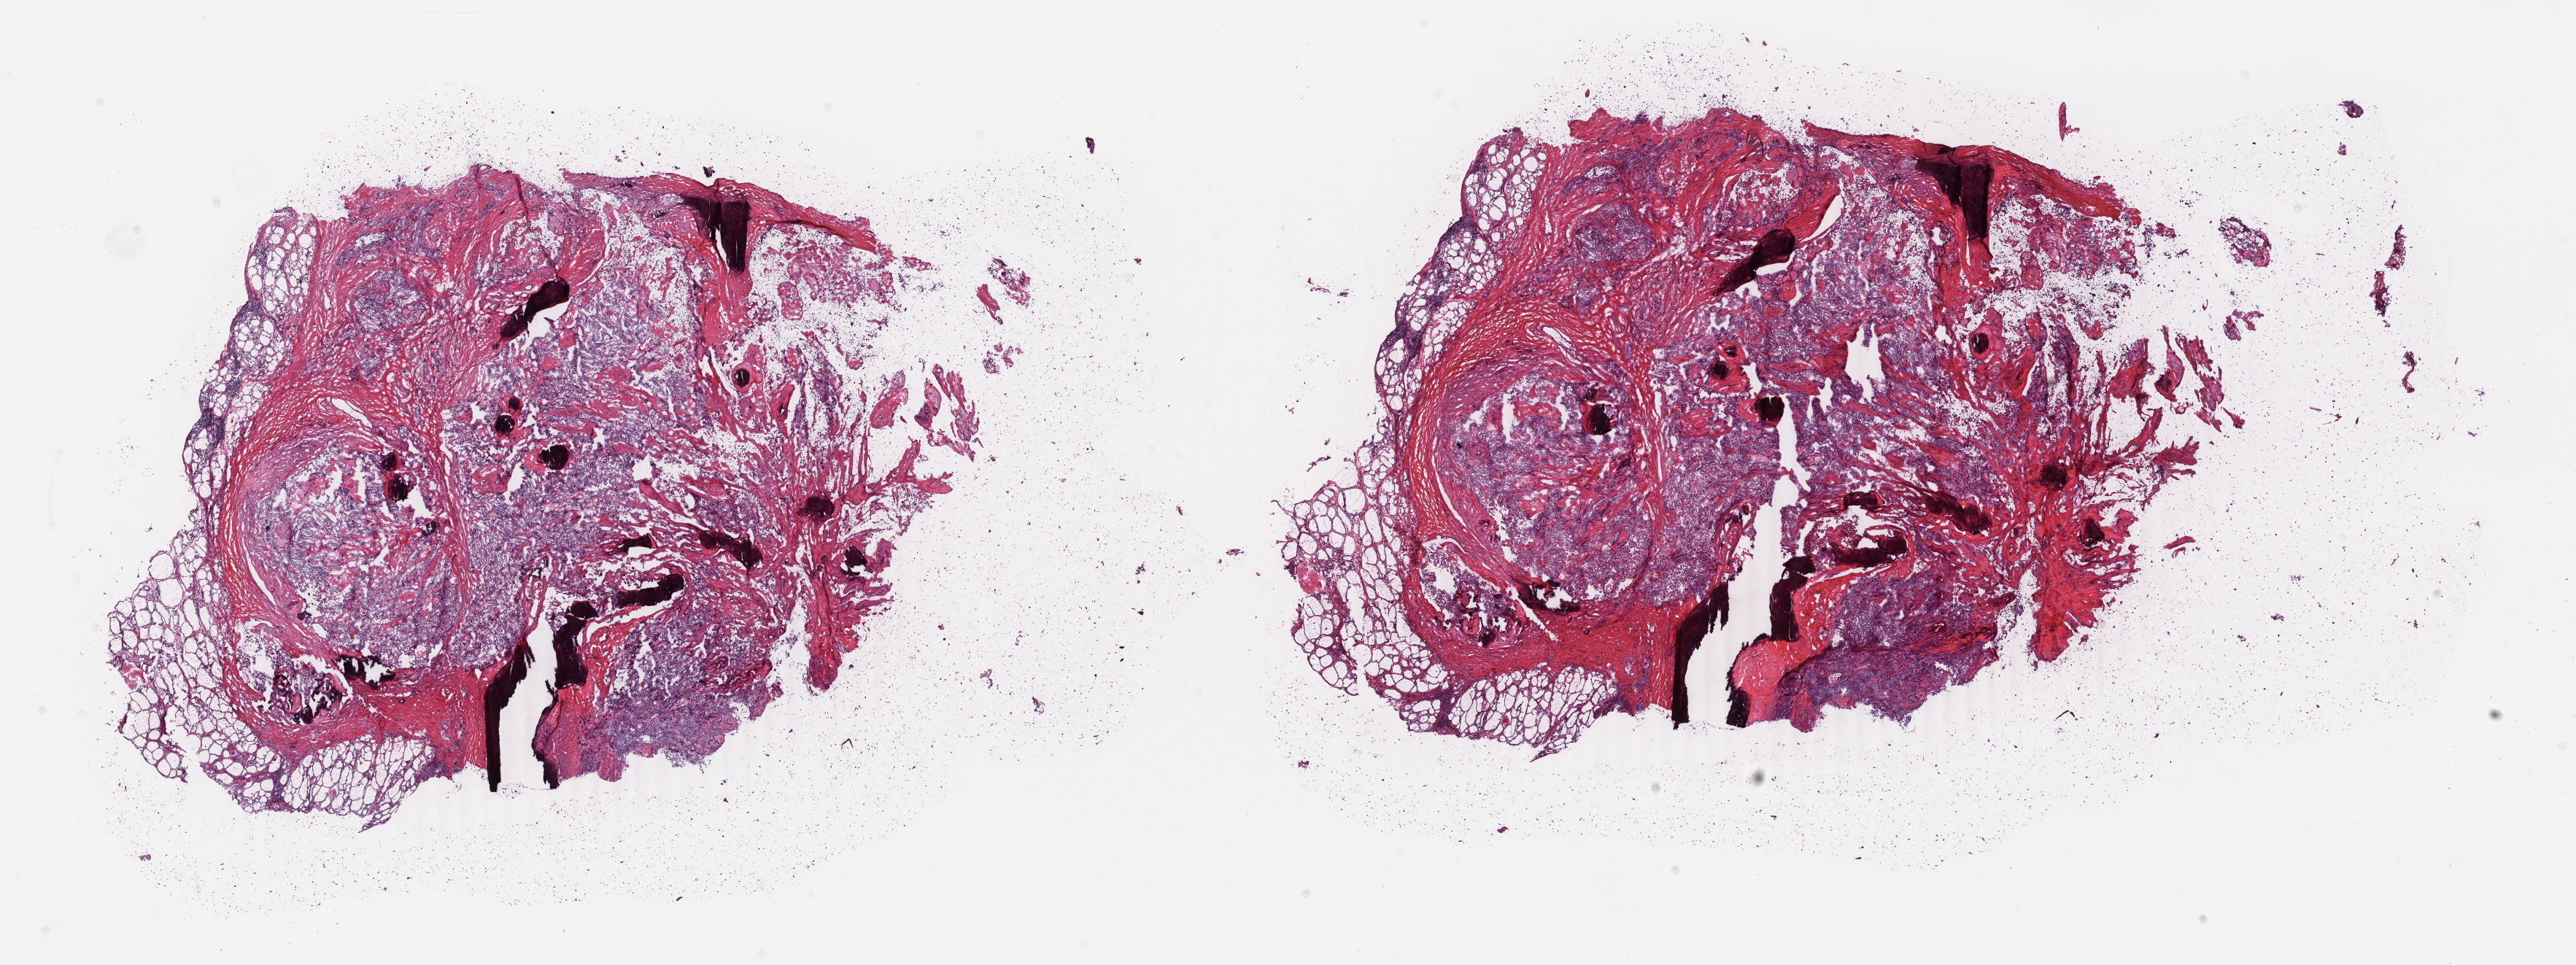
Hematoxylin and eosin (H&E) stained whole-slide image — a low-resolution overview of the entire scanned area, about 28.1 x 10.5 mm; frozen section; sample: primary tumour, thyroid. Patient: male, age at initial diagnosis 56 years. Composition of this section per pathologist review: tumour cells 85%, tumour nuclei 70%, normal cells 10%, stromal cells 5%, necrosis 0%. Infiltration values recorded for this section: lymphocyte infiltration 0%, monocyte infiltration 0%, neutrophil infiltration 0%.
* lymph nodes positive (case pathology): 0 of 6 examined
* AJCC pathologic stage: I
* diagnosis: Papillary adenocarcinoma, NOS (thyroid gland)
* laterality: right